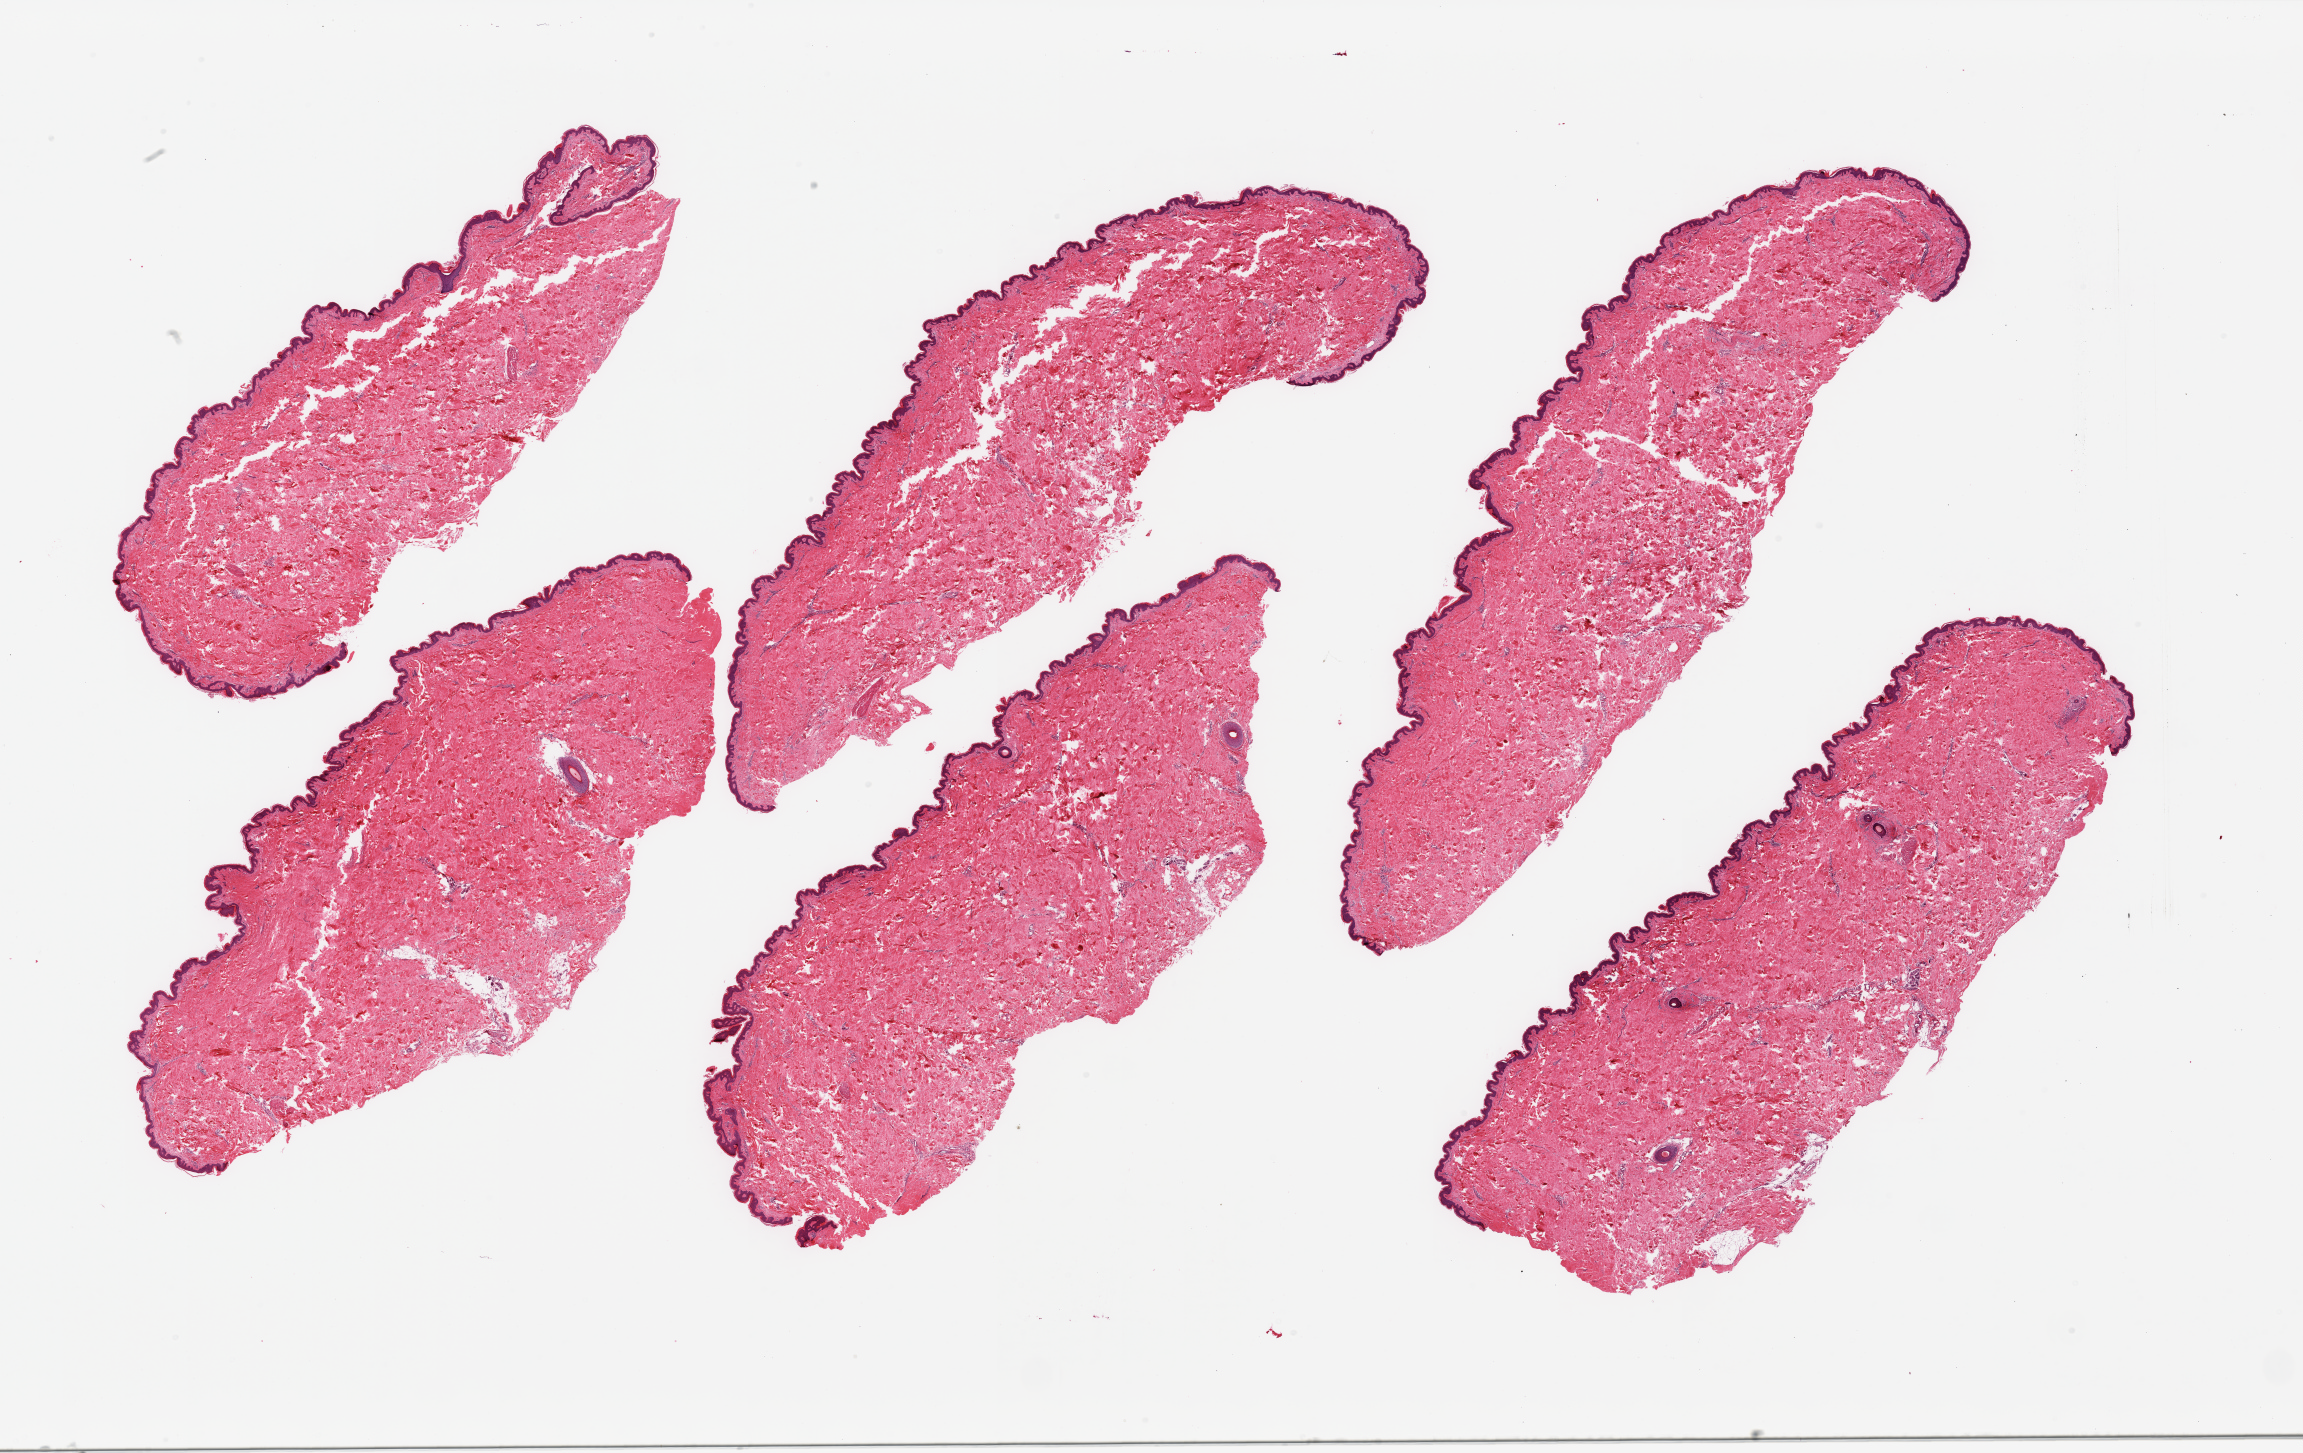
Digitized H&E-stained section — whole scanned area (about 36.4 x 23.0 mm, acquisition: 20x scan) shown as a low-resolution overview, PAXgene-fixed, paraffin-embedded tissue, section of skin of suprapubic region (target tissue), donor tissue sample. Donor sex: male.
- pathologist's review note for this sample: 6 pieces; dermal cracks